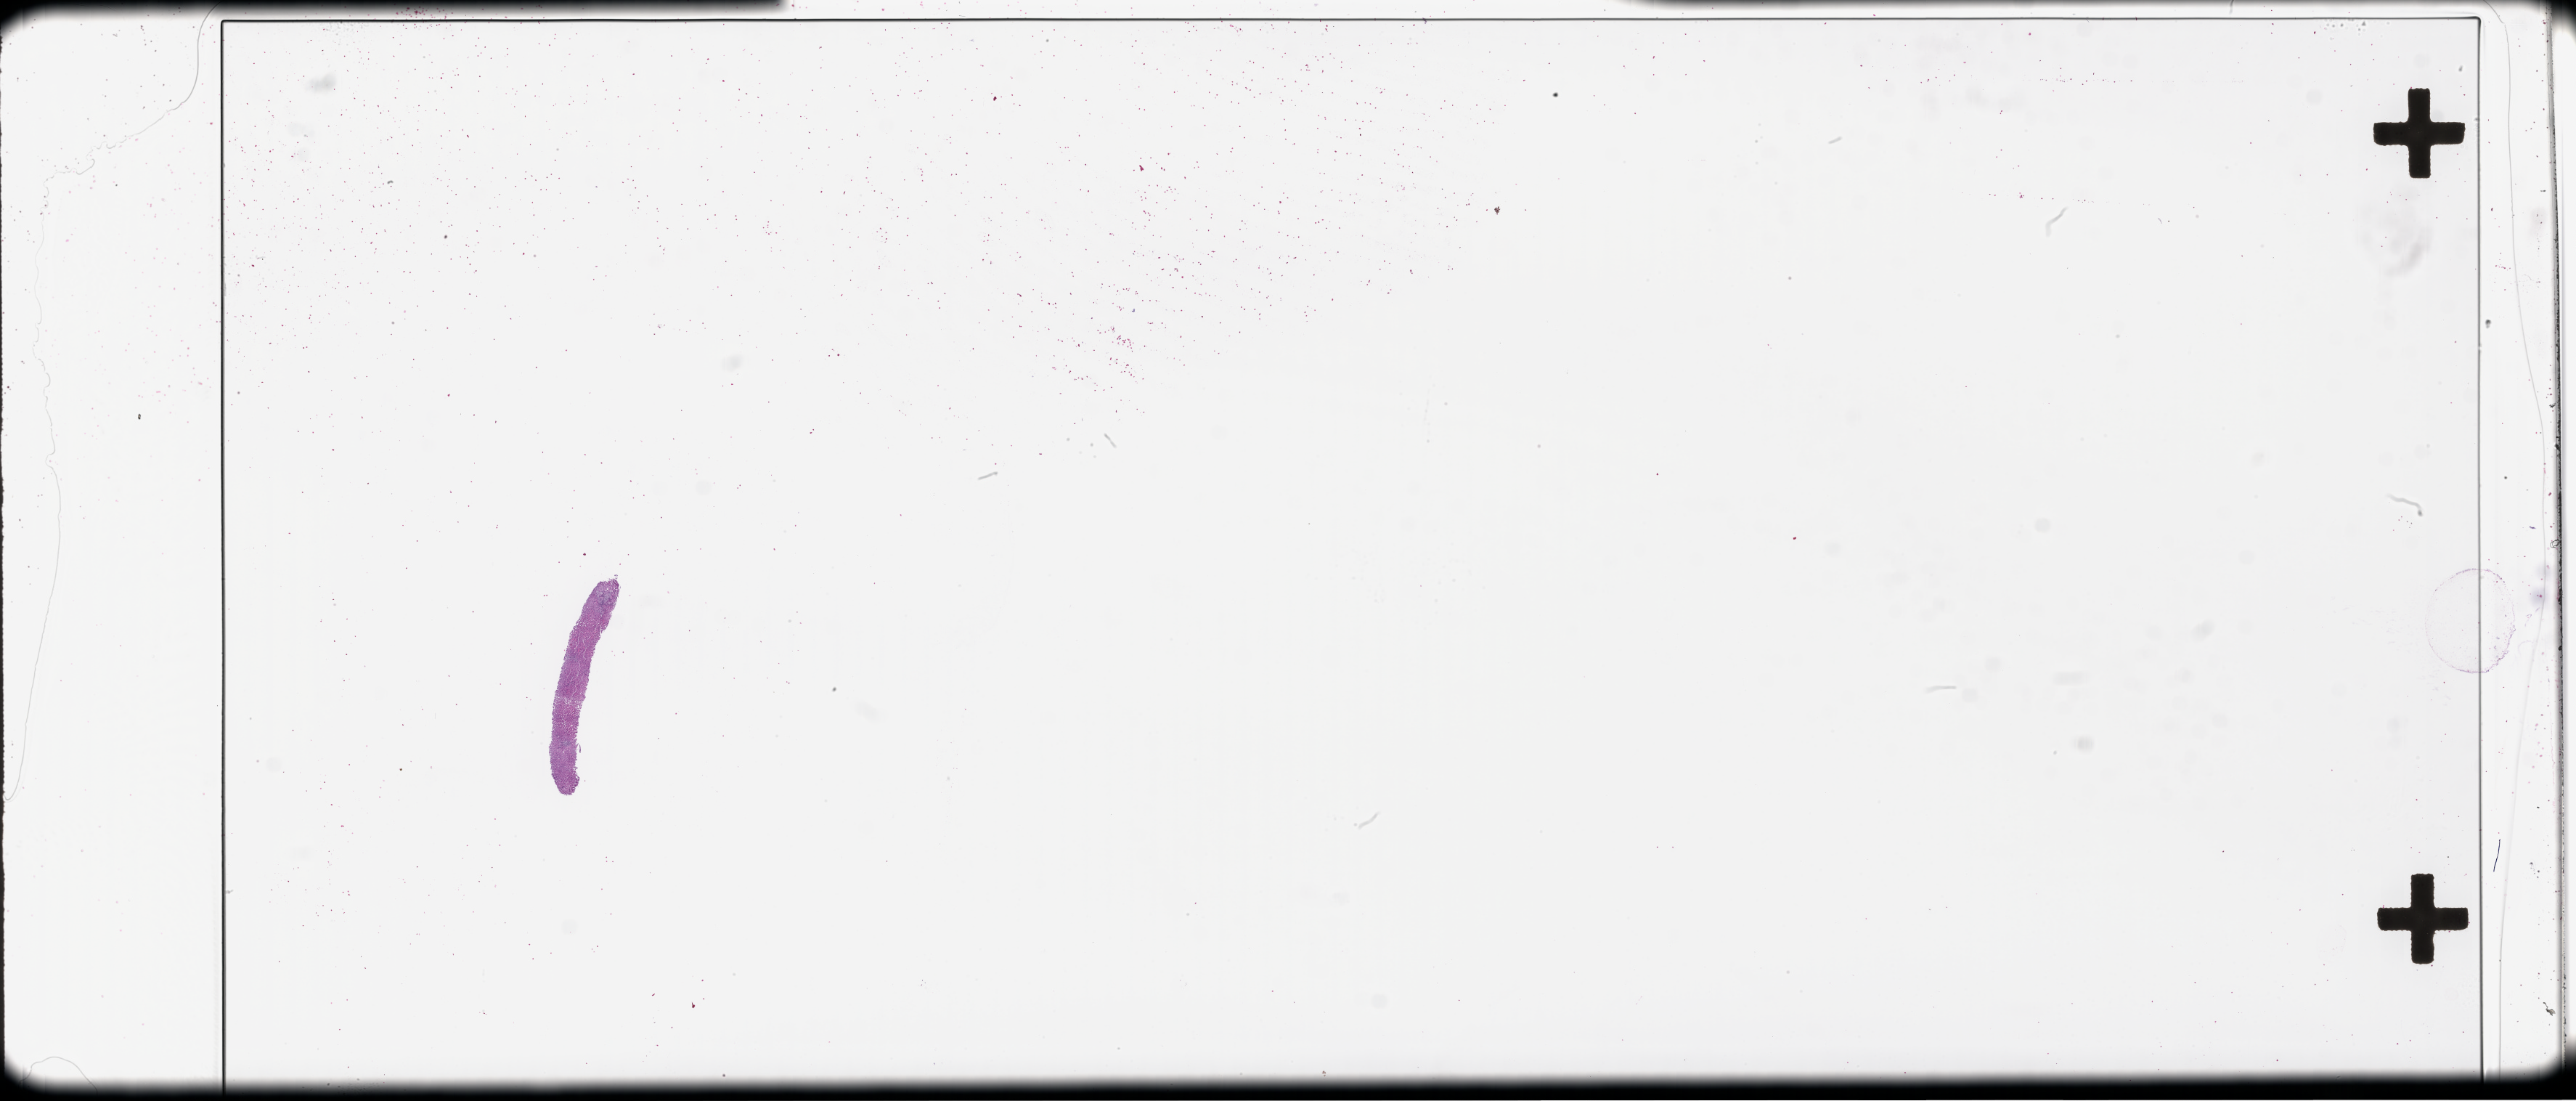
Whole-slide image, hematoxylin and eosin (H&E) stain — shown as a low-resolution overview of the whole scanned area (about 57.3 x 24.5 mm); FFPE section; collected at baseline (before treatment). Patient: male.
- this section: metastatic tumor tissue
- primary diagnosis of the patient: Colorectal Carcinoma